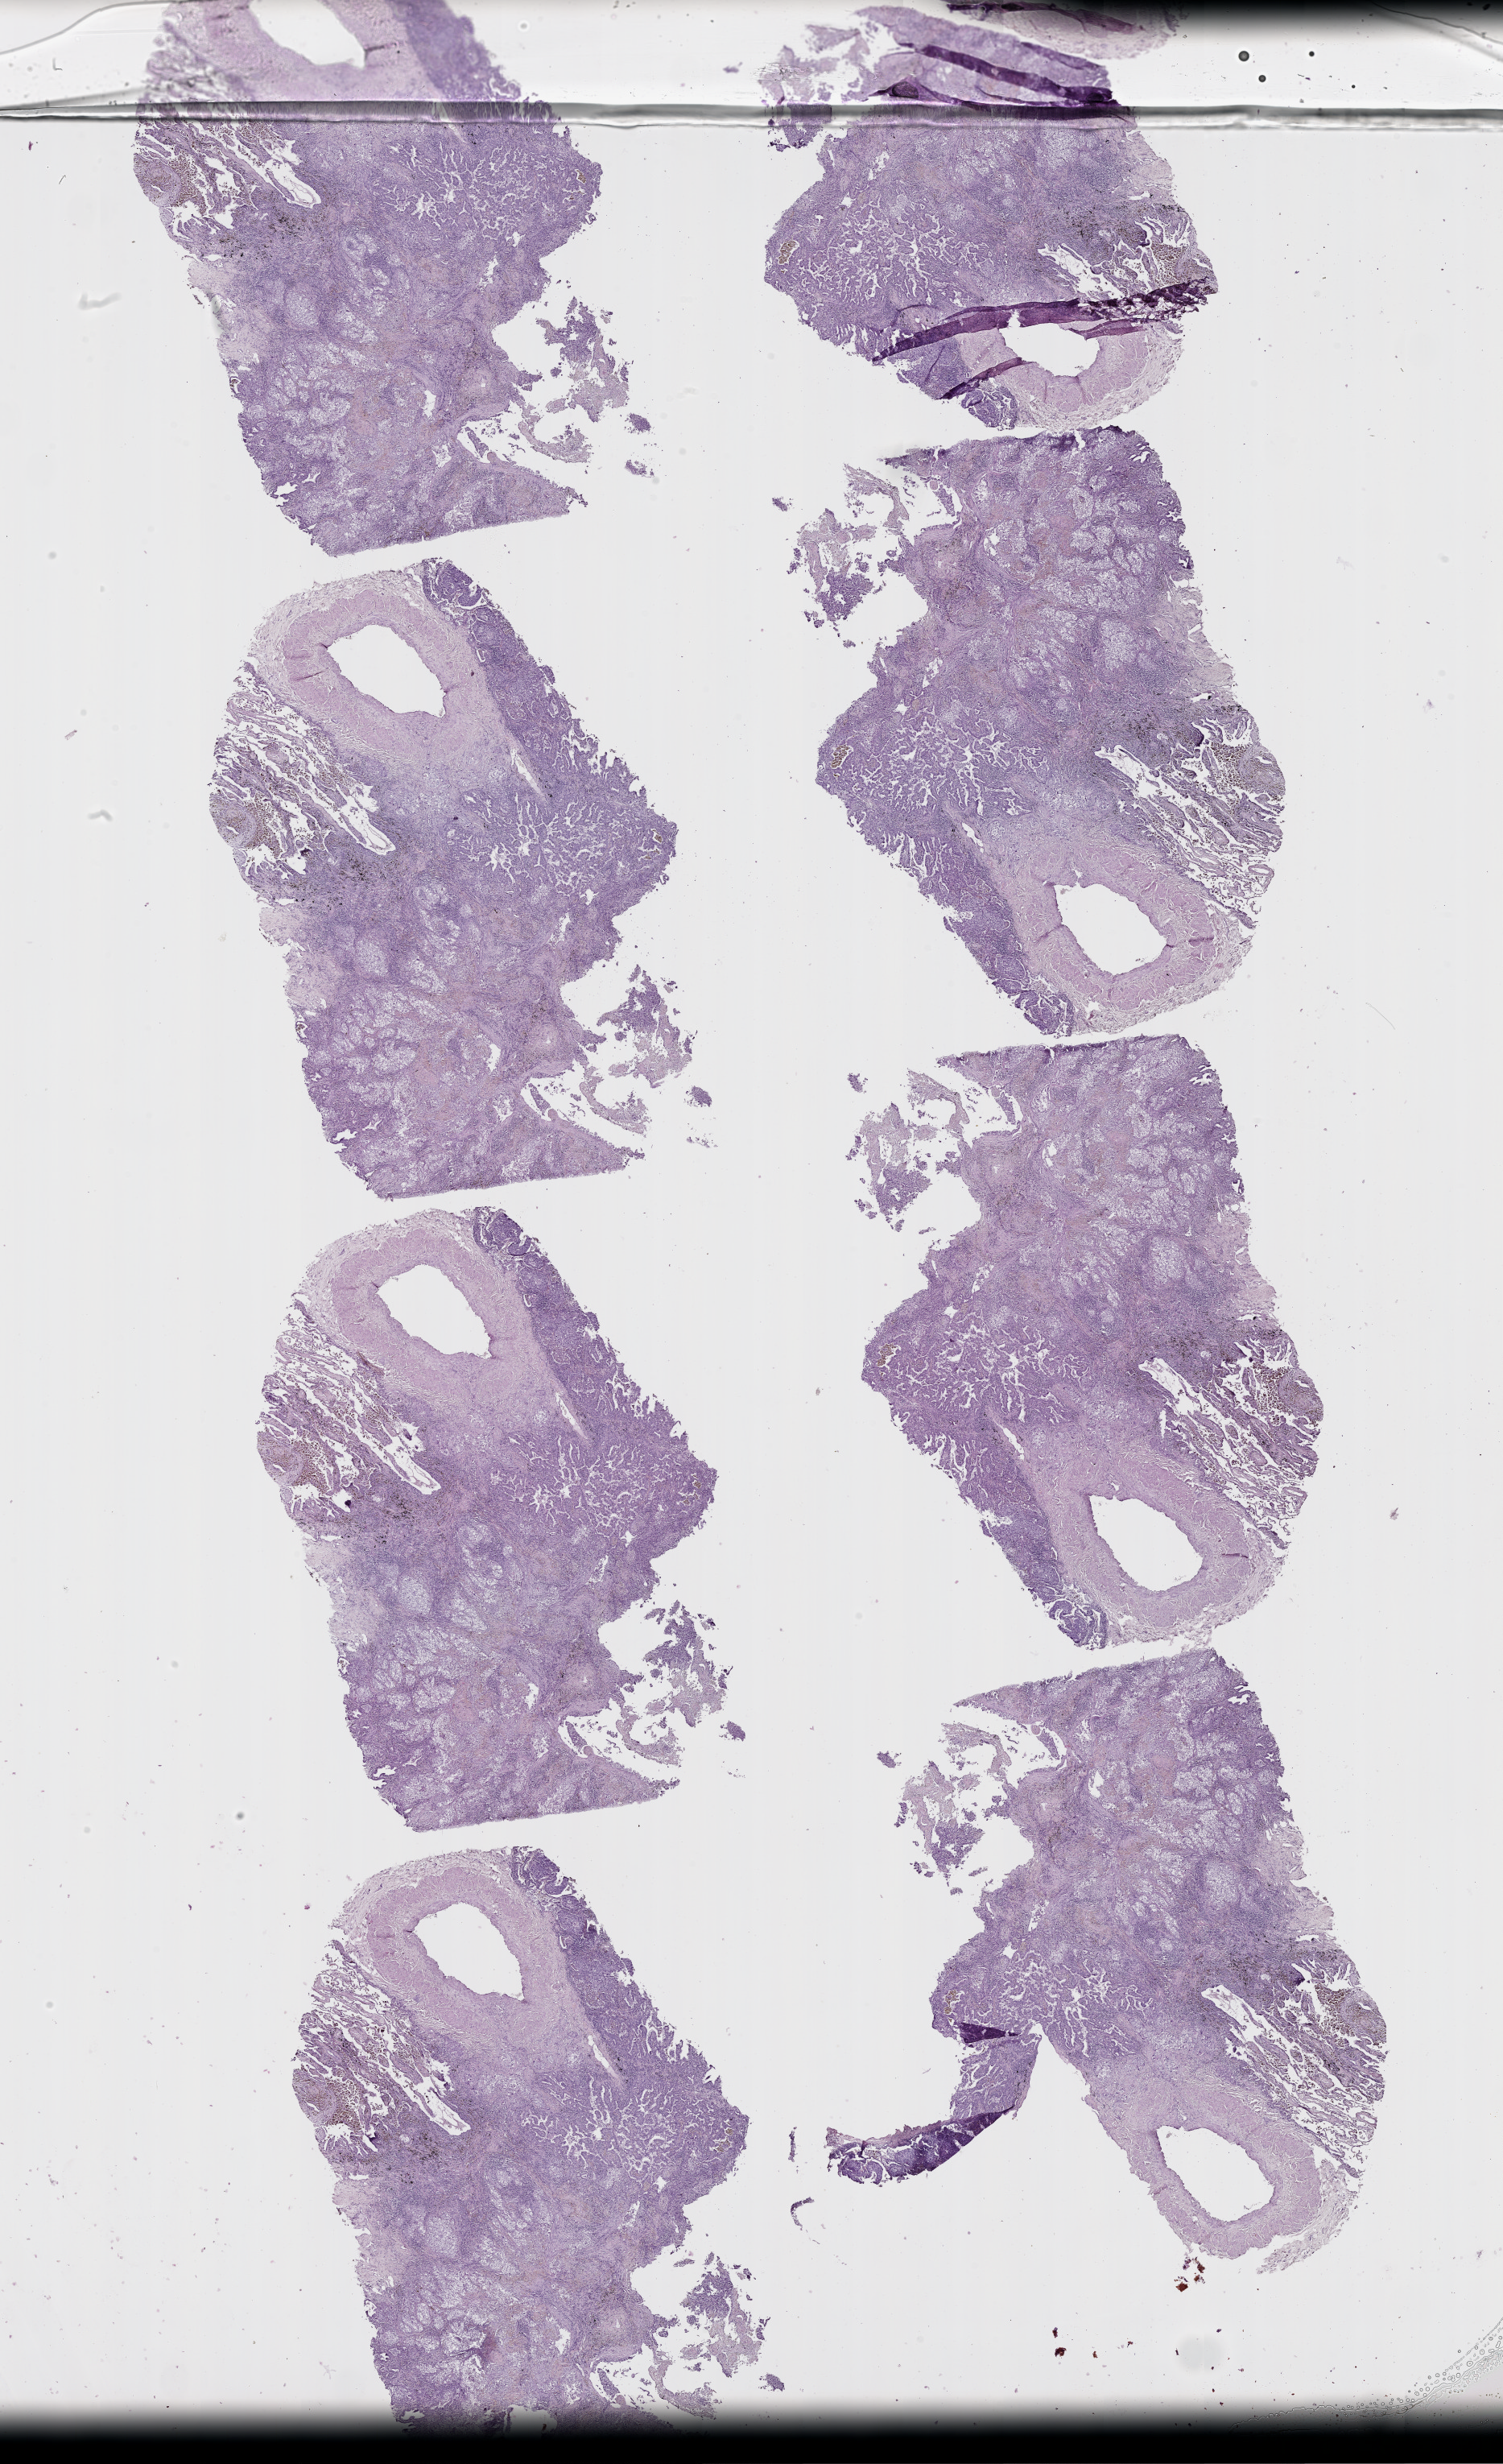
H&E-stained whole-slide image — a low-resolution overview of the entire scanned area, about 15.0 x 24.6 mm (from a 20x scan); lung, tissue type not recorded.
Patient diagnosis (cohort enrolment): lung adenocarcinoma (lung).